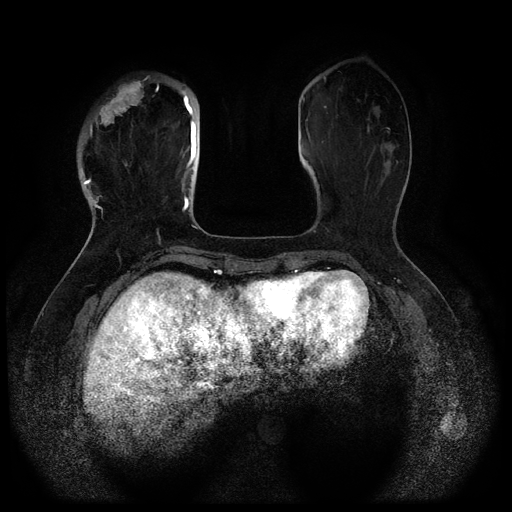
Breast MRI (dynamic contrast-enhanced, multi-phase), one axial slice. Position 29 of 116 along the scan axis. Dynamic contrast-enhanced series, time point 2 of 5 at this slice position (early post-contrast). 1.5 T. TE 2.6 ms, TR 5.3 ms. 2 mm slice thickness. 512 × 512 image matrix, field of view 350 × 350 mm. Female patient, age 51 years.
Structures marked on this image (semi-automatic segmentation, software-assisted and operator-edited):
- breast lesion (labelled 'tumour' in the annotation; benign lesions carry a separate 'benign' label): box from (x=97, y=80) to (x=145, y=131) px